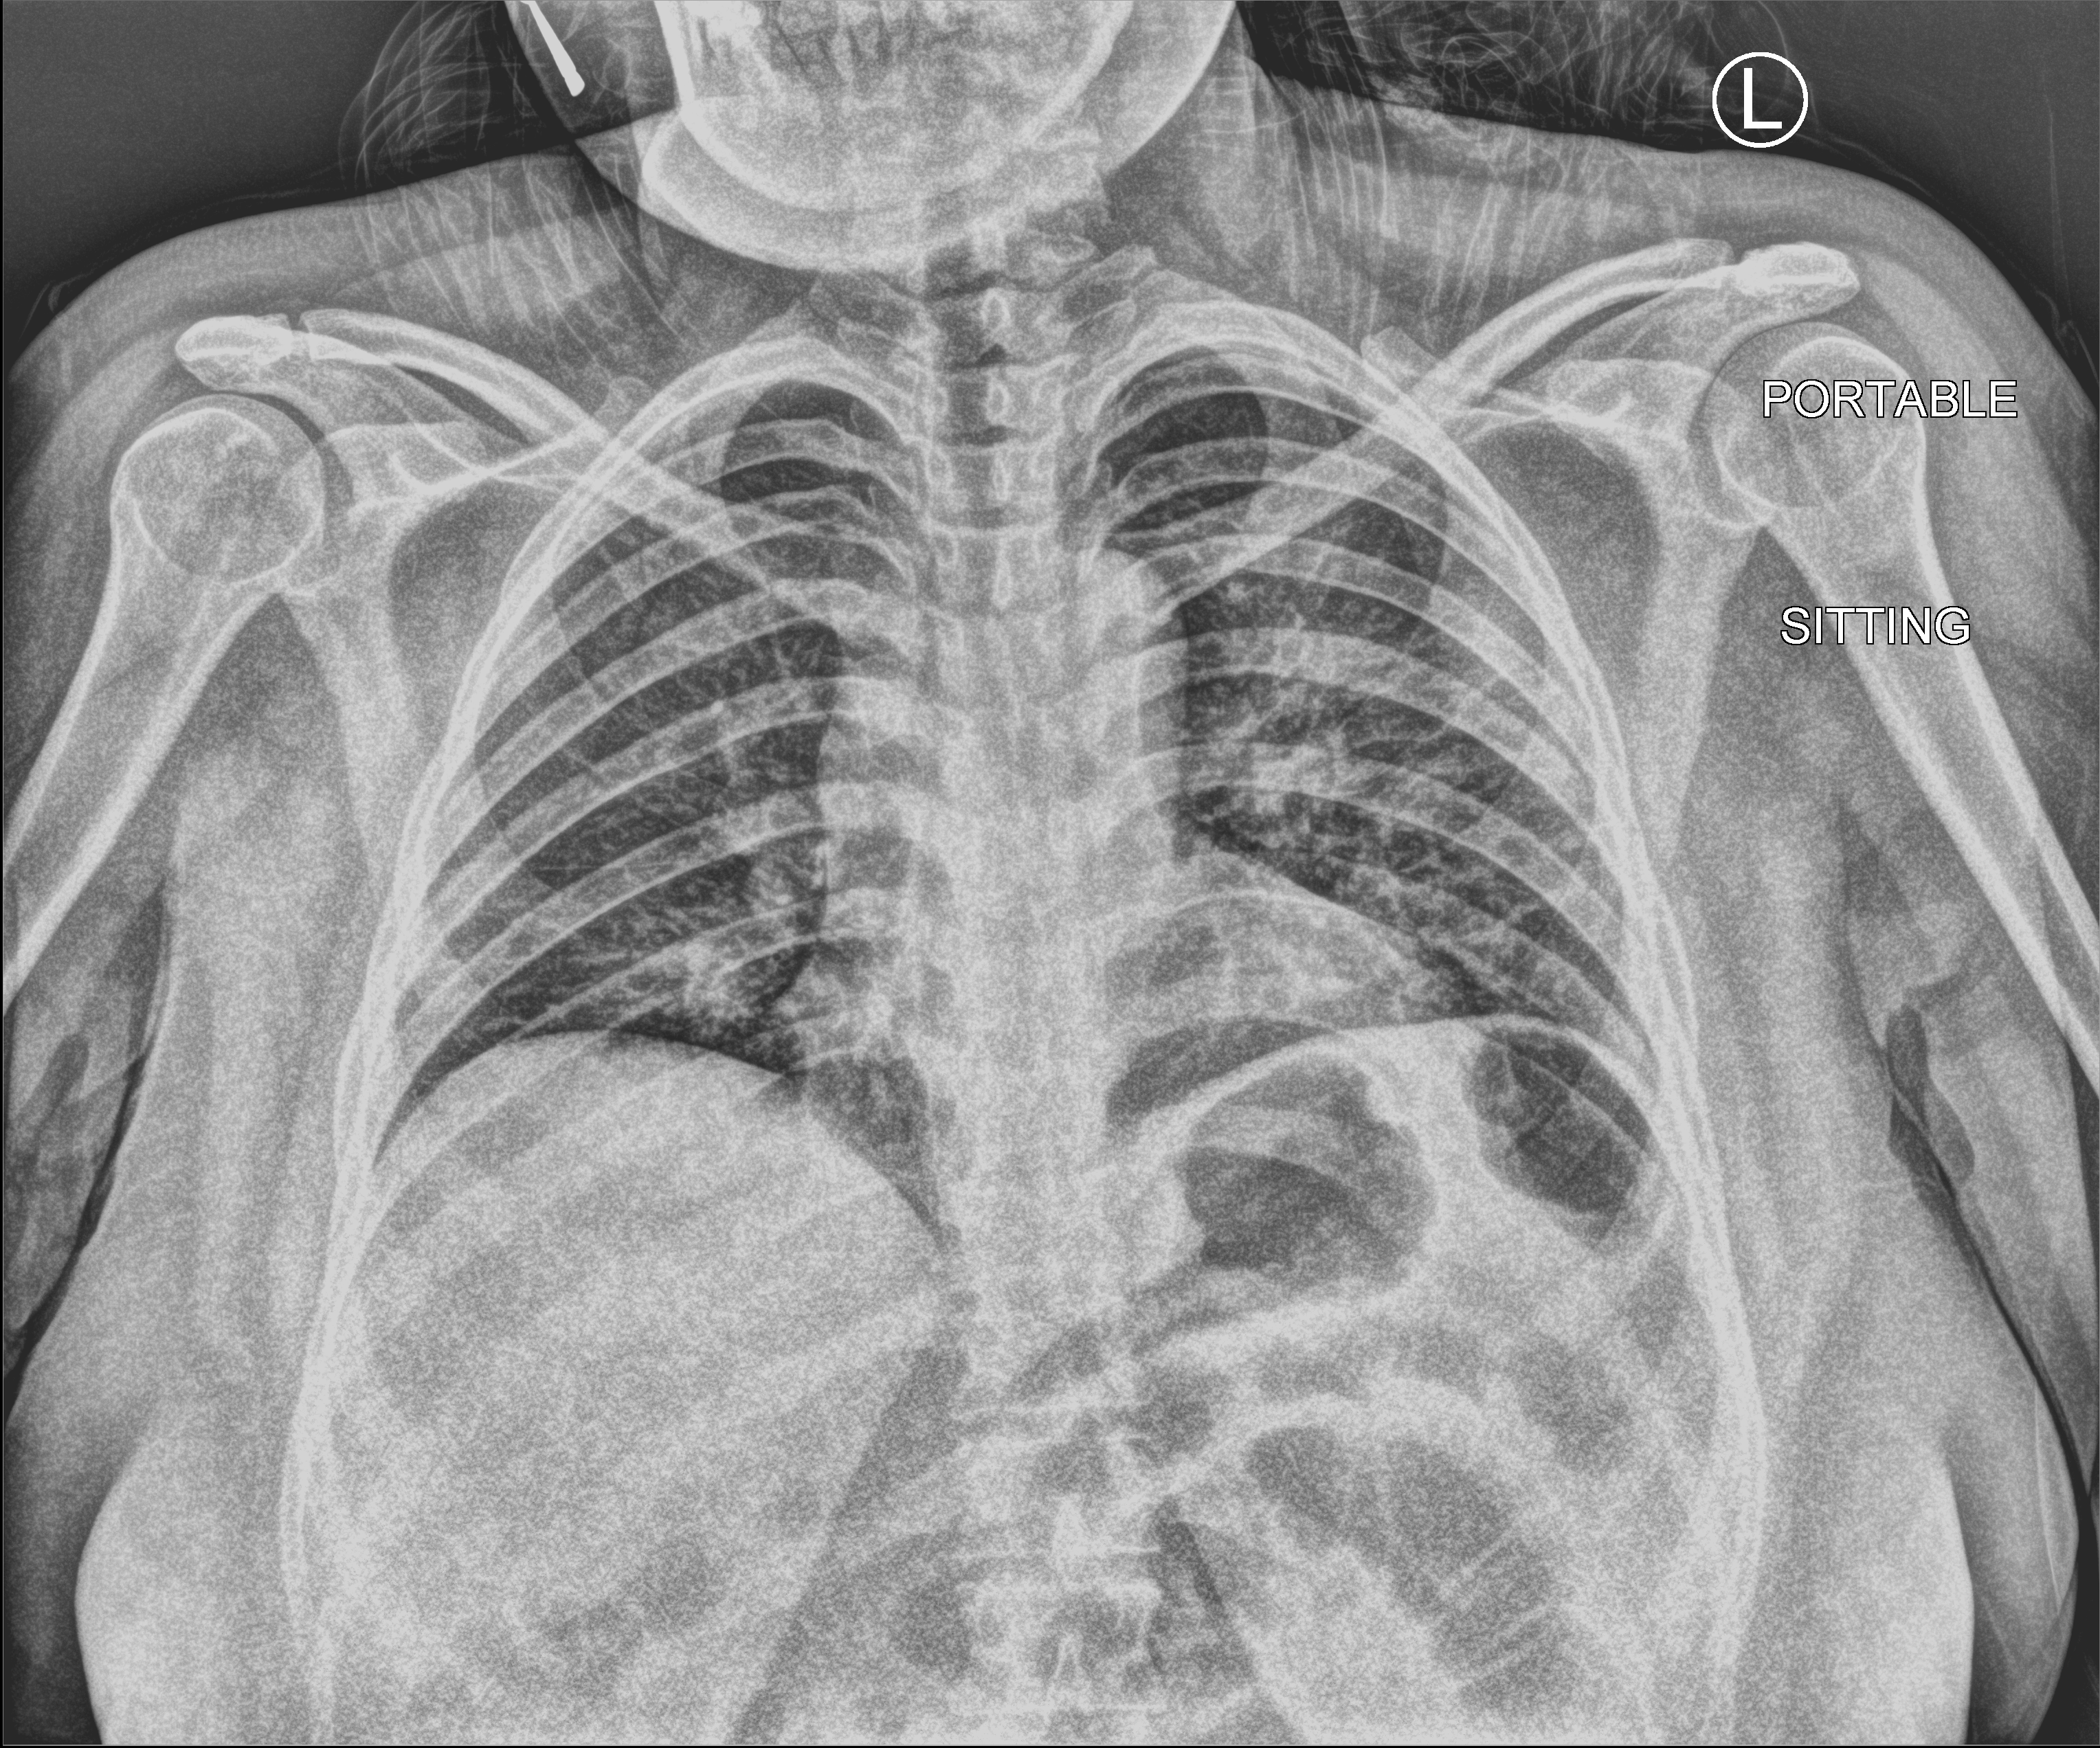
Bedside chest radiograph (computed radiography), anteroposterior (AP) projection. Patient hospitalised with COVID-19; female, aged 18–59 years.
Admission-level facts for this patient (not findings on this image; timing relative to this image not recorded):
- length of hospital stay: 1 day
- mechanically ventilated during this hospital stay: no
- admitted to intensive care during this hospital stay: no